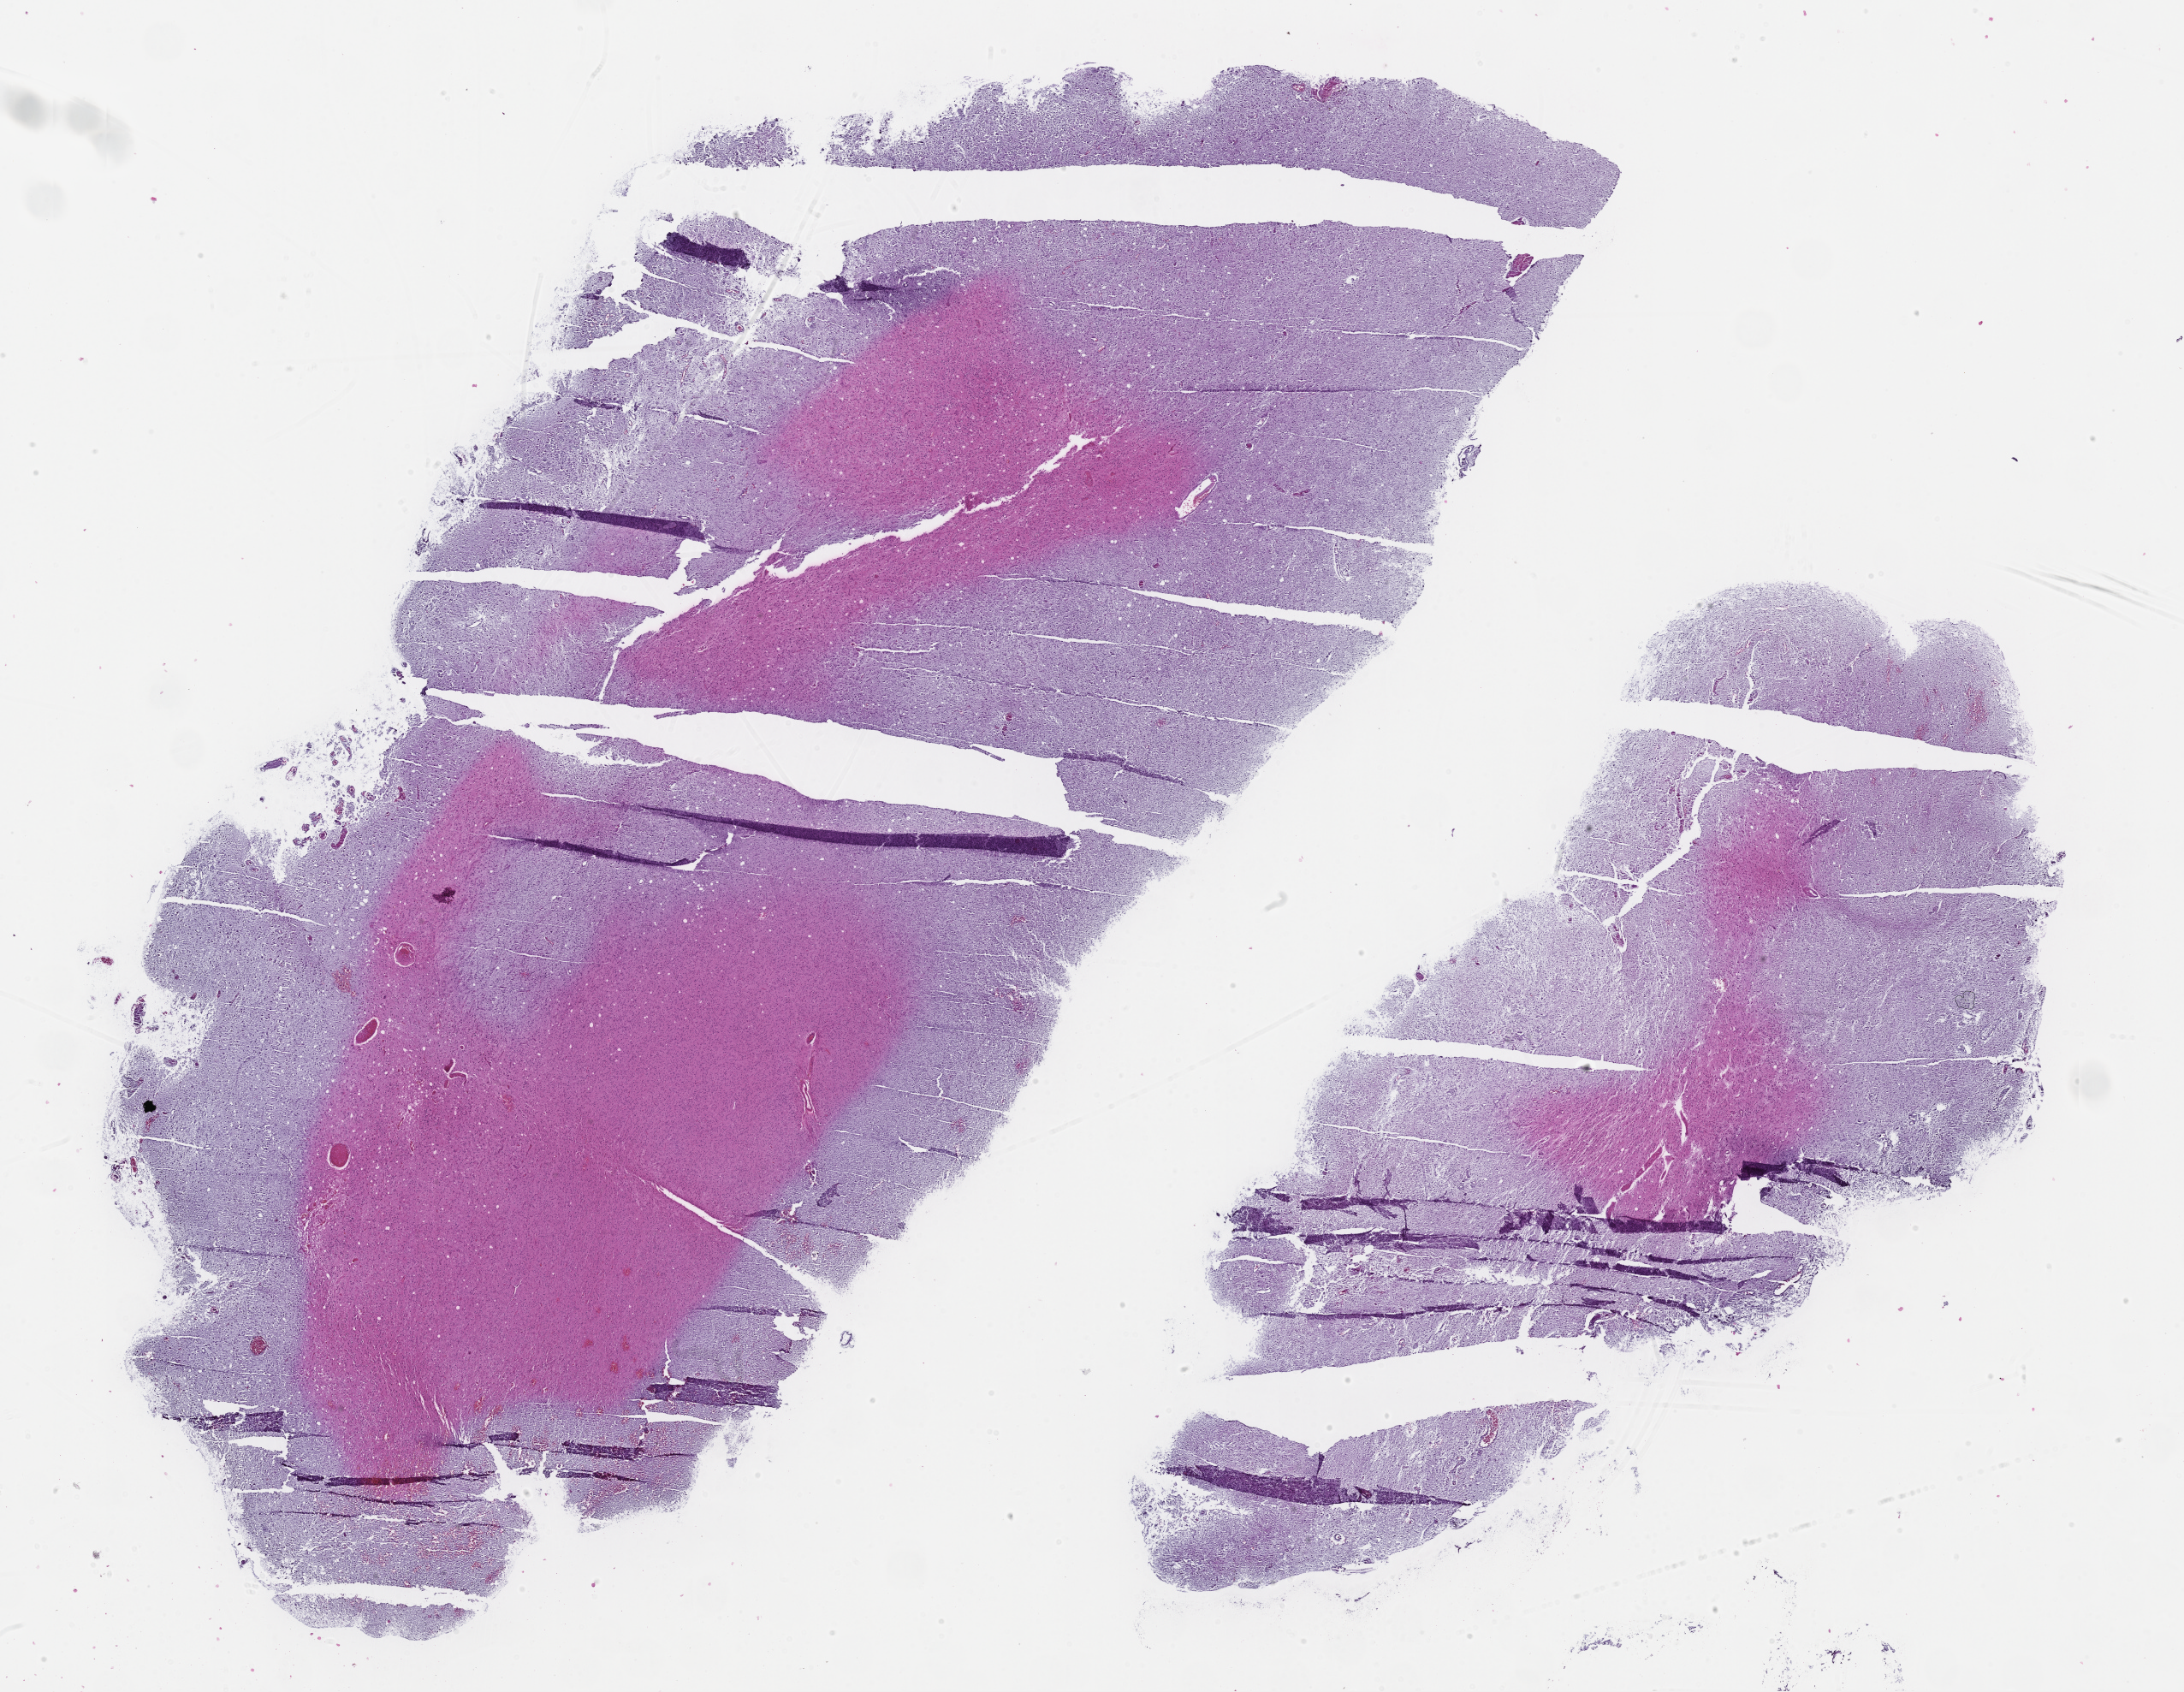
Whole-slide histology image, H&E-stained — a low-resolution overview of the entire scanned area, about 20.7 x 16.0 mm (slide scanned at 40x); FFPE section; brain, primary tumour sample. Female patient; age at initial diagnosis 70 years.
- pathologic diagnosis: Glioblastoma